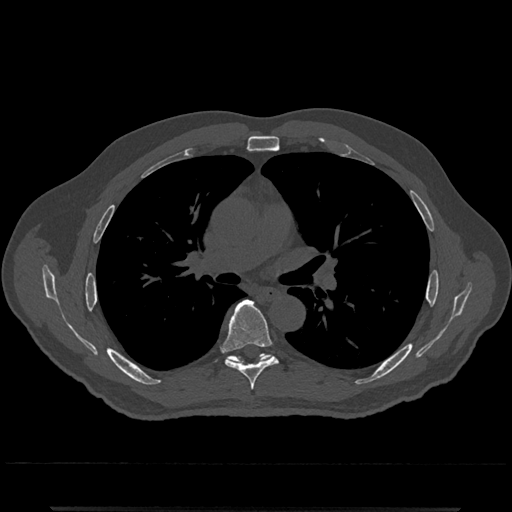
CT including the spine, one axial slice; slice 764 of 797 in the series (ordered by position); bone window (W 1800 / L 400 HU); 0.5 mm slice thickness; 512 × 512 image matrix. Patient: male, 67 years. From the clinical record (not read from this slice): primary cancer: prostate.
Annotated regions visible in this slice (semi-automatic segmentation, software-assisted and operator-edited):
- T6 vertebra: bounding box <221,300,278,390> (left, top, right, bottom; pixels)
- T7 vertebra: <227,354,271,364>